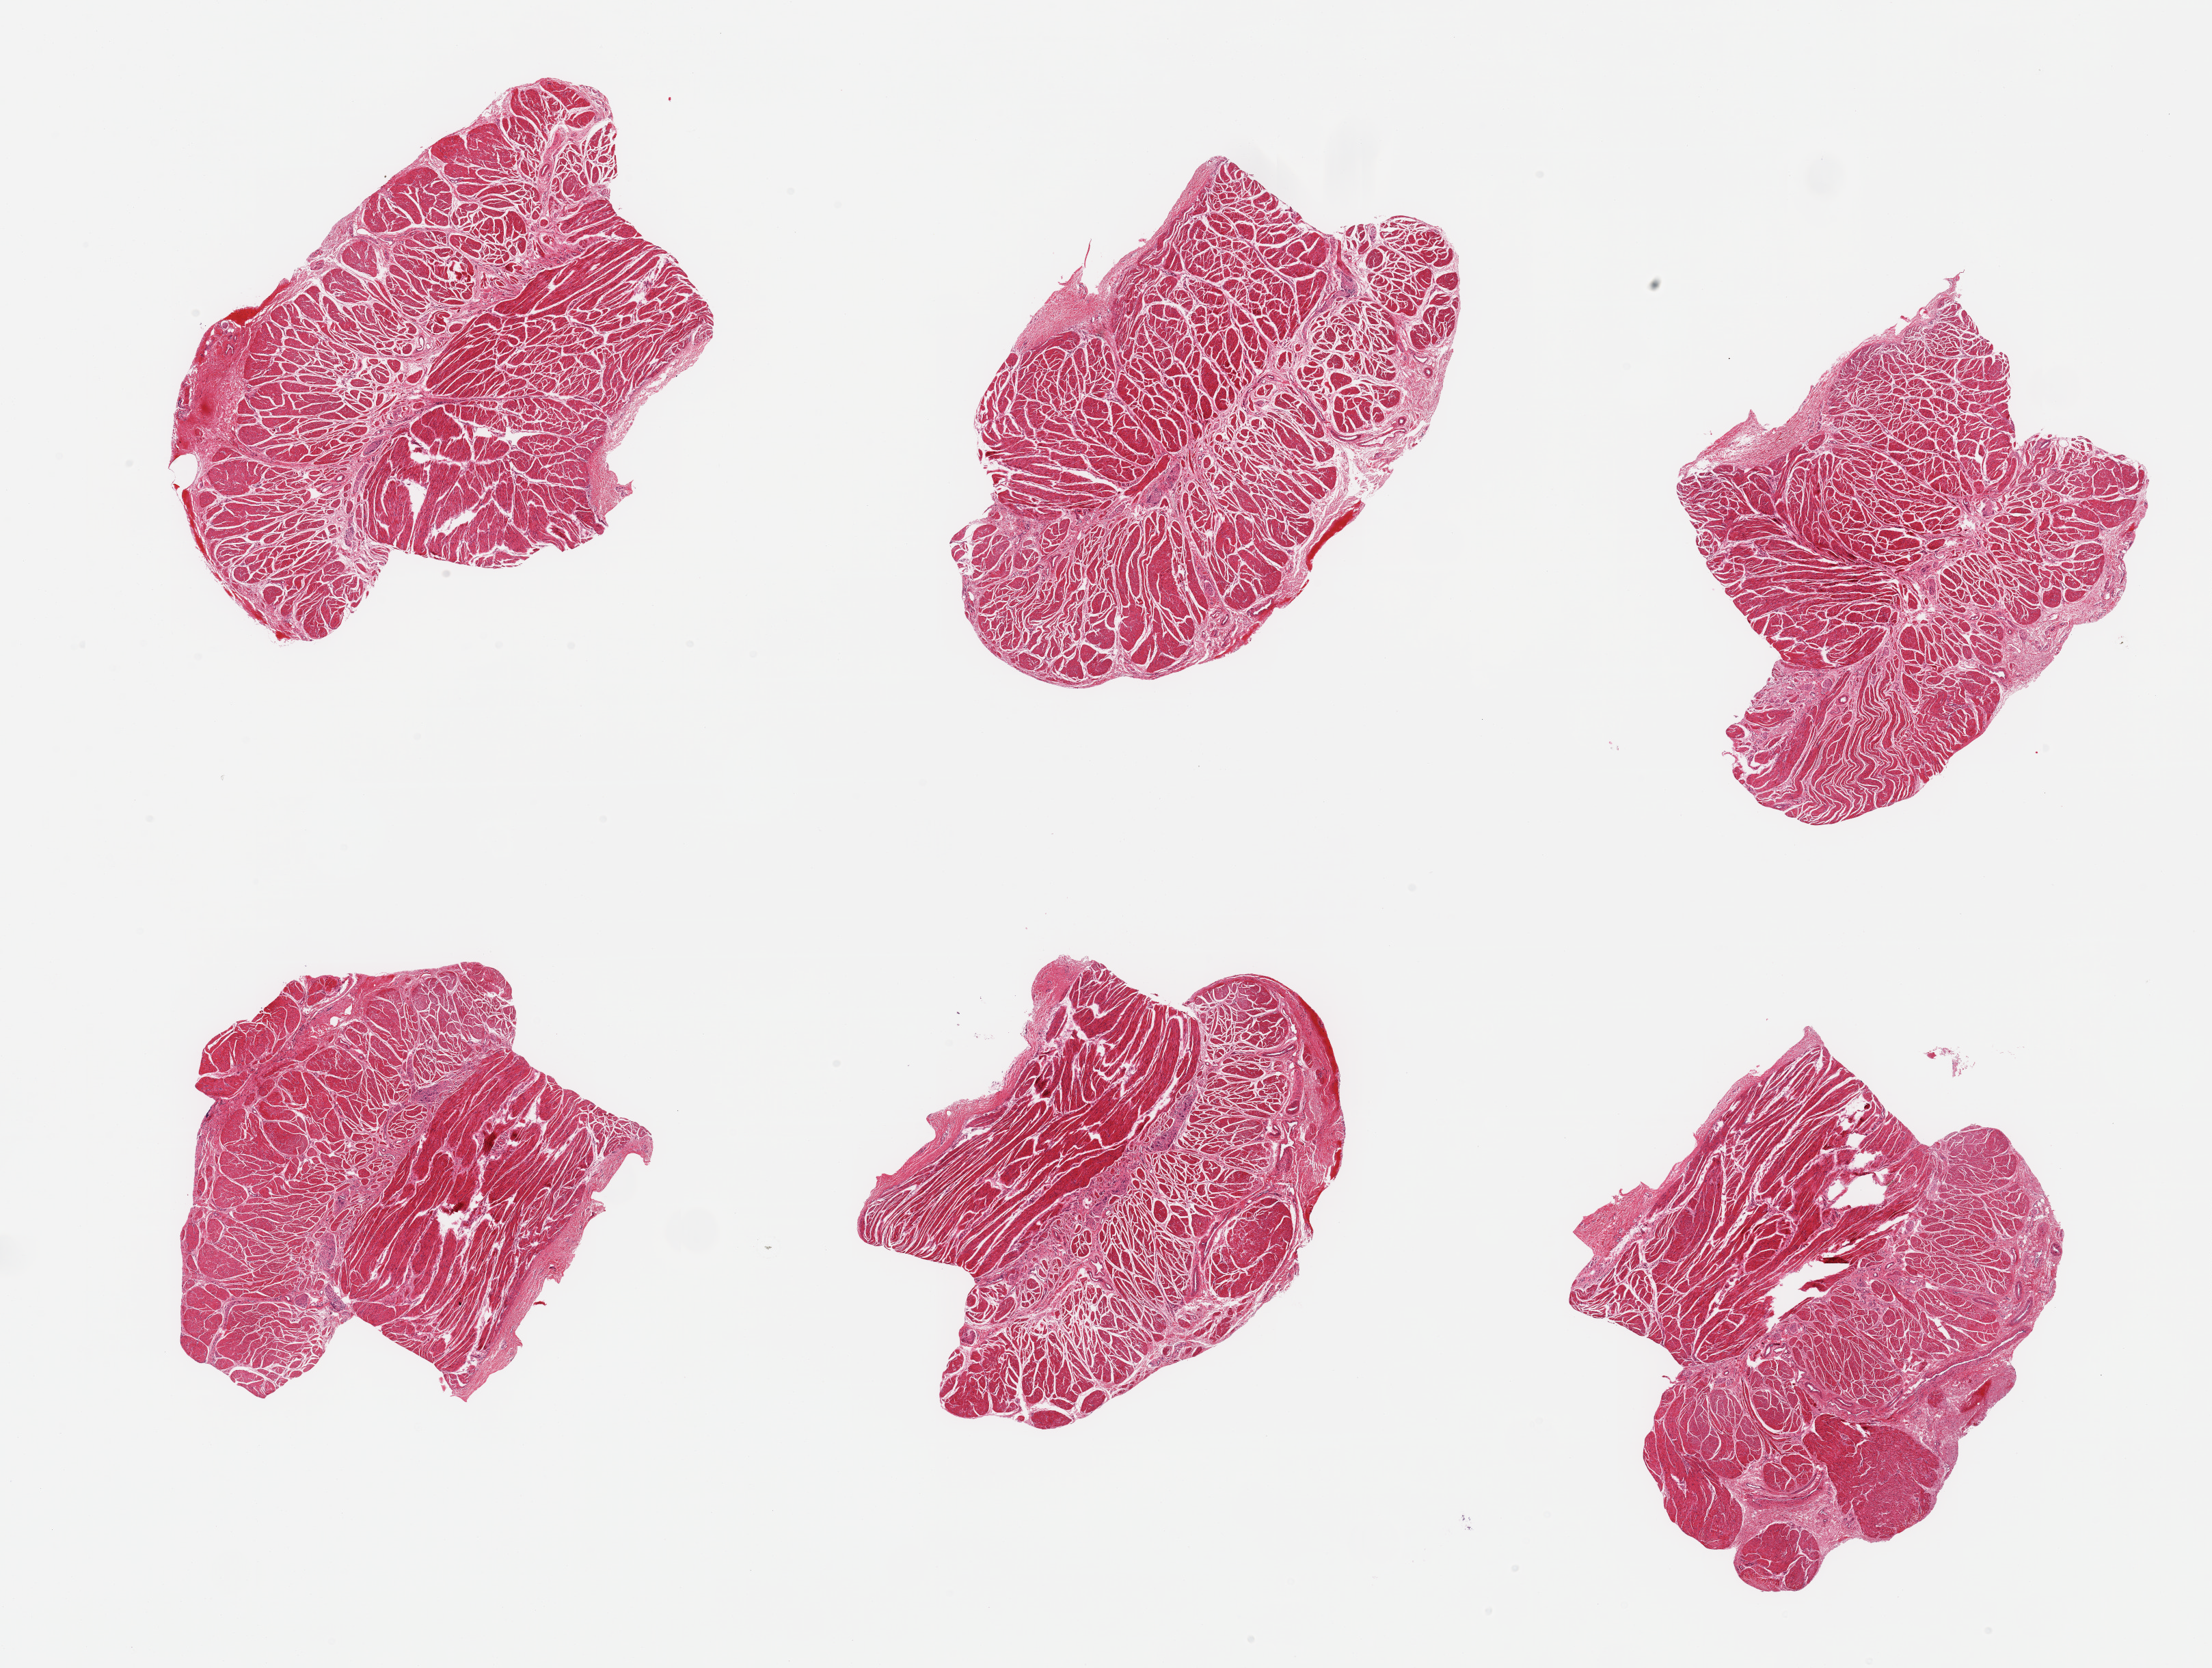
Digitized hematoxylin and eosin (H&E)-stained section, a low-resolution overview of the entire scanned area, about 25.6 x 19.3 mm (acquisition: 20x scan). PAXgene-fixed, paraffin-embedded tissue. Target tissue: gastroesophageal junction. Donor tissue sample. Male donor.
Reviewer comment on this tissue sample: 6 pieces; target muscularis.